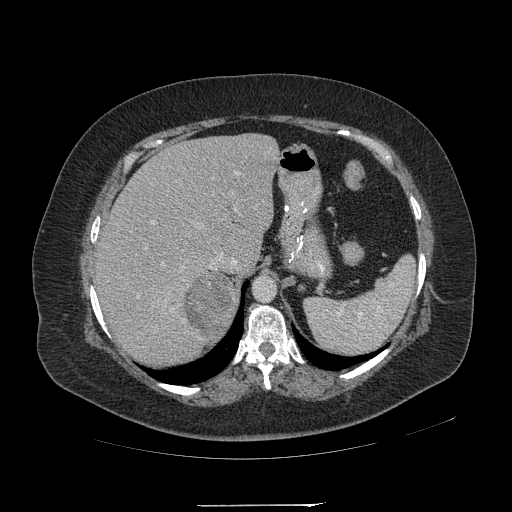
Contrast-enhanced abdominal CT, one axial slice; slice 159 of 217 in the series (ordered by position); reconstruction kernel STANDARD; 120 kVp; intravenous contrast given; soft-tissue window (W 400 / L 40 HU); 1.25 mm slice thickness; 512 × 512 image matrix, field of view 453 × 453 mm. Female patient, age 55 years. From the clinical record (not read from this slice): diagnosis: adrenocortical carcinoma; tumour side: right adrenal; tumour size at pathology: 11 cm; Ki-67 index: 20 %; stage (as recorded): 2.
Annotated regions visible in this slice (semi-automatic segmentation, software-assisted and operator-edited):
- mass: bounding box <184,274,234,338> (left, top, right, bottom; pixels)